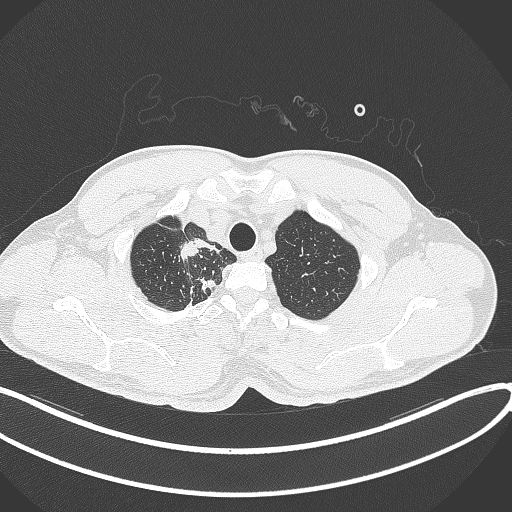
Chest CT, one axial slice. Slice 333 of 391 in the series (ordered by position). Reconstruction kernel B70f. Lung window (W 1500 / L -600 HU). 512 × 512 image matrix. Male patient, age 48 years. Case-level facts recorded for this patient, not image findings: clinical TNM (as recorded): T1c N1 M1.
Outlined on this slice (rectangle marked by the reading radiologist):
- lung tumour (recorded histology: adenocarcinoma): box from (x=175, y=236) to (x=201, y=261) px